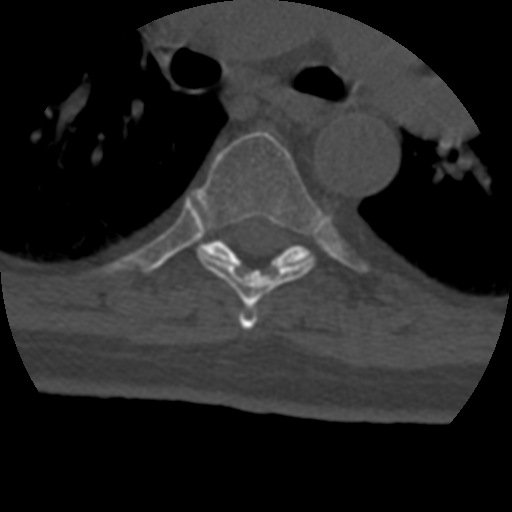
CT including the spine, one axial slice. Slice 295 of 399 in the series (ordered by position). Reconstruction kernel STANDARD. 120 kVp. Bone window (W 1800 / L 400 HU). 1.25 mm slice thickness. 512 × 512 image matrix, field of view 160 × 160 mm. Patient age 69 years. From the clinical record (not read from this slice): primary cancer: prostate.
Annotated regions visible in this slice (semi-automatically segmented with operator editing):
- T5 vertebra: bounding box <239,308,258,330> (left, top, right, bottom; pixels)
- T6 vertebra: <197,131,322,307>
- T7 vertebra: <205,239,311,268>